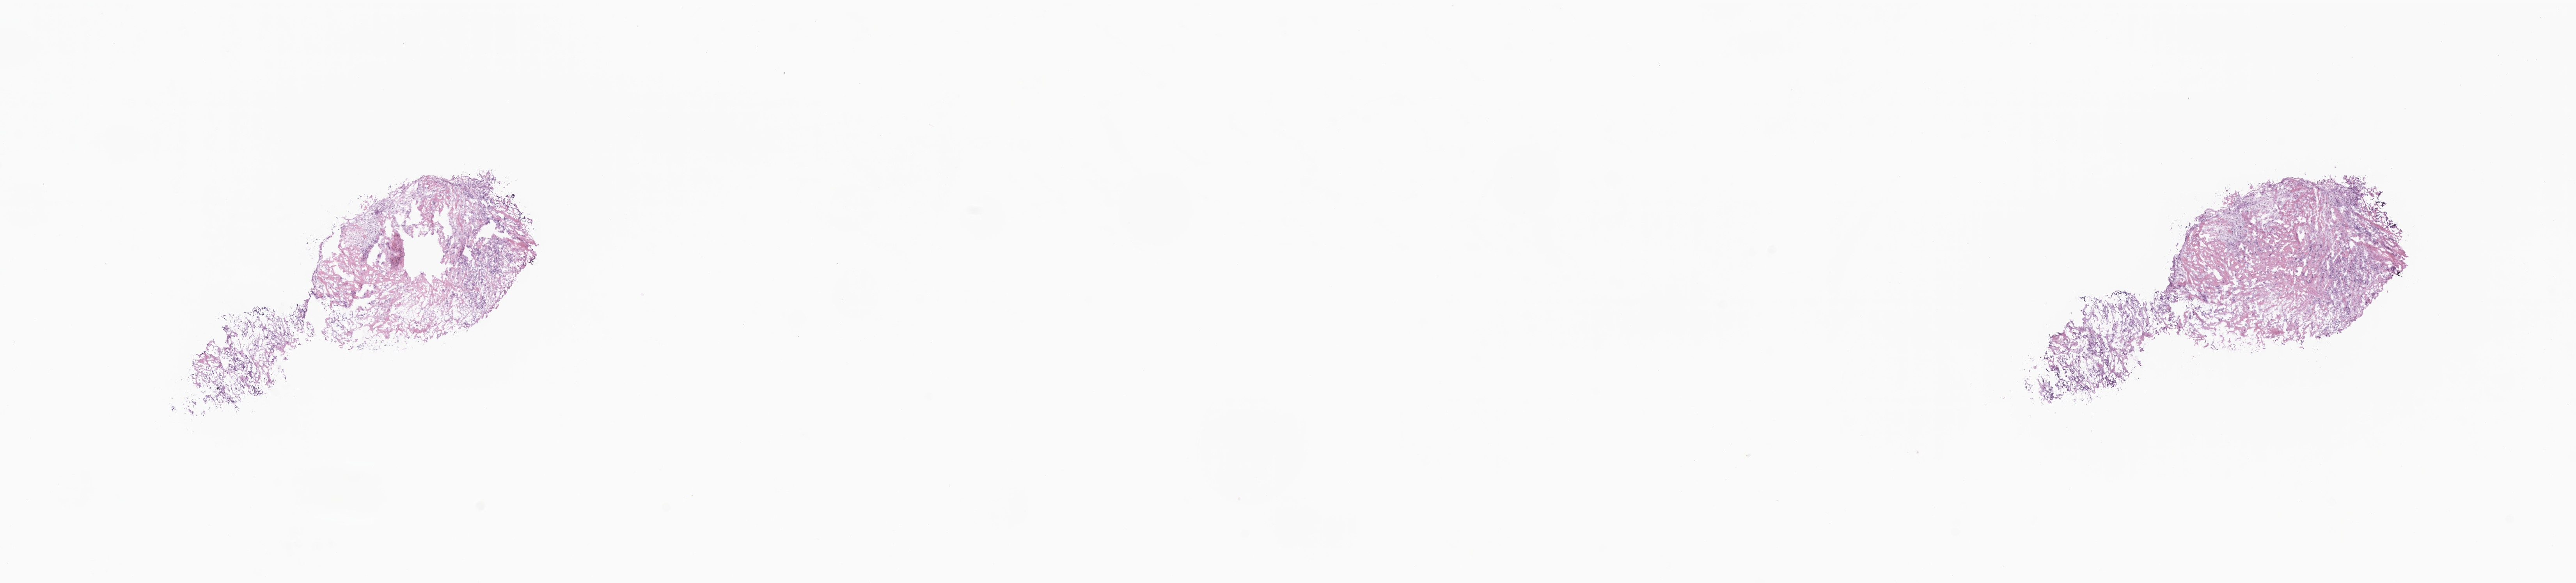
Haematoxylin and eosin whole-slide image, a low-resolution overview of the entire scanned area, about 27.8 x 6.3 mm, cryosection, primary tumor, site: breast. Female, age 51 years at initial diagnosis. Composition of this section per pathologist review: tumor cells 50%, tumor nuclei 80%, stromal cells 25%, necrosis 25%, normal cells 0%. Inflammatory infiltration, as recorded: lymphocyte infiltration 0%, monocyte infiltration 0%, neutrophil infiltration 0%.
* histologic diagnosis: Infiltrating duct carcinoma, NOS
* section: top of the tissue portion